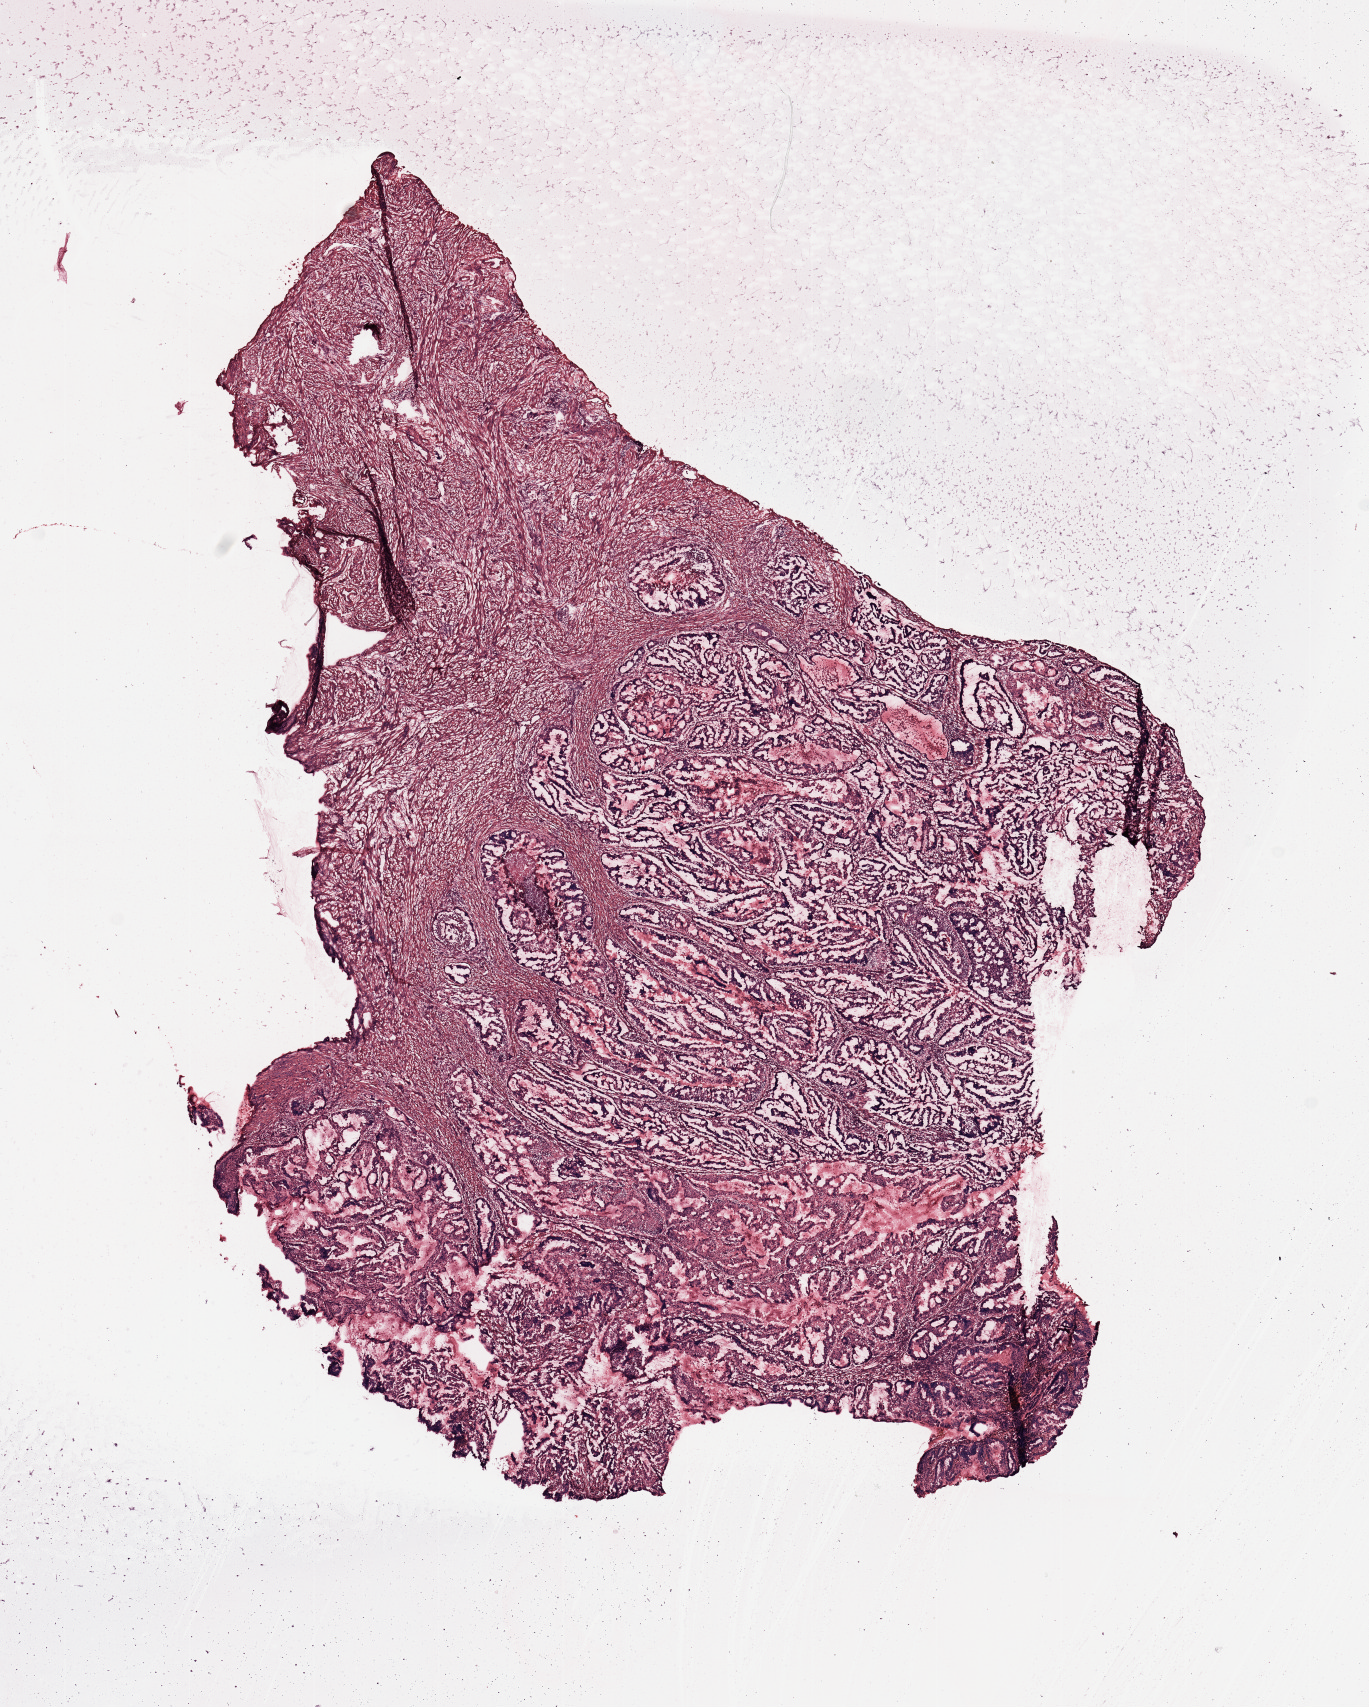
Digitized H&E-stained tissue section (whole slide), shown as a low-resolution overview of the whole scanned area (about 10.8 x 13.5 mm). Tumour tissue sample, uterus. Patient: female, age 68 years.
Histologic diagnosis: Endometrioid adenocarcinoma, NOS.